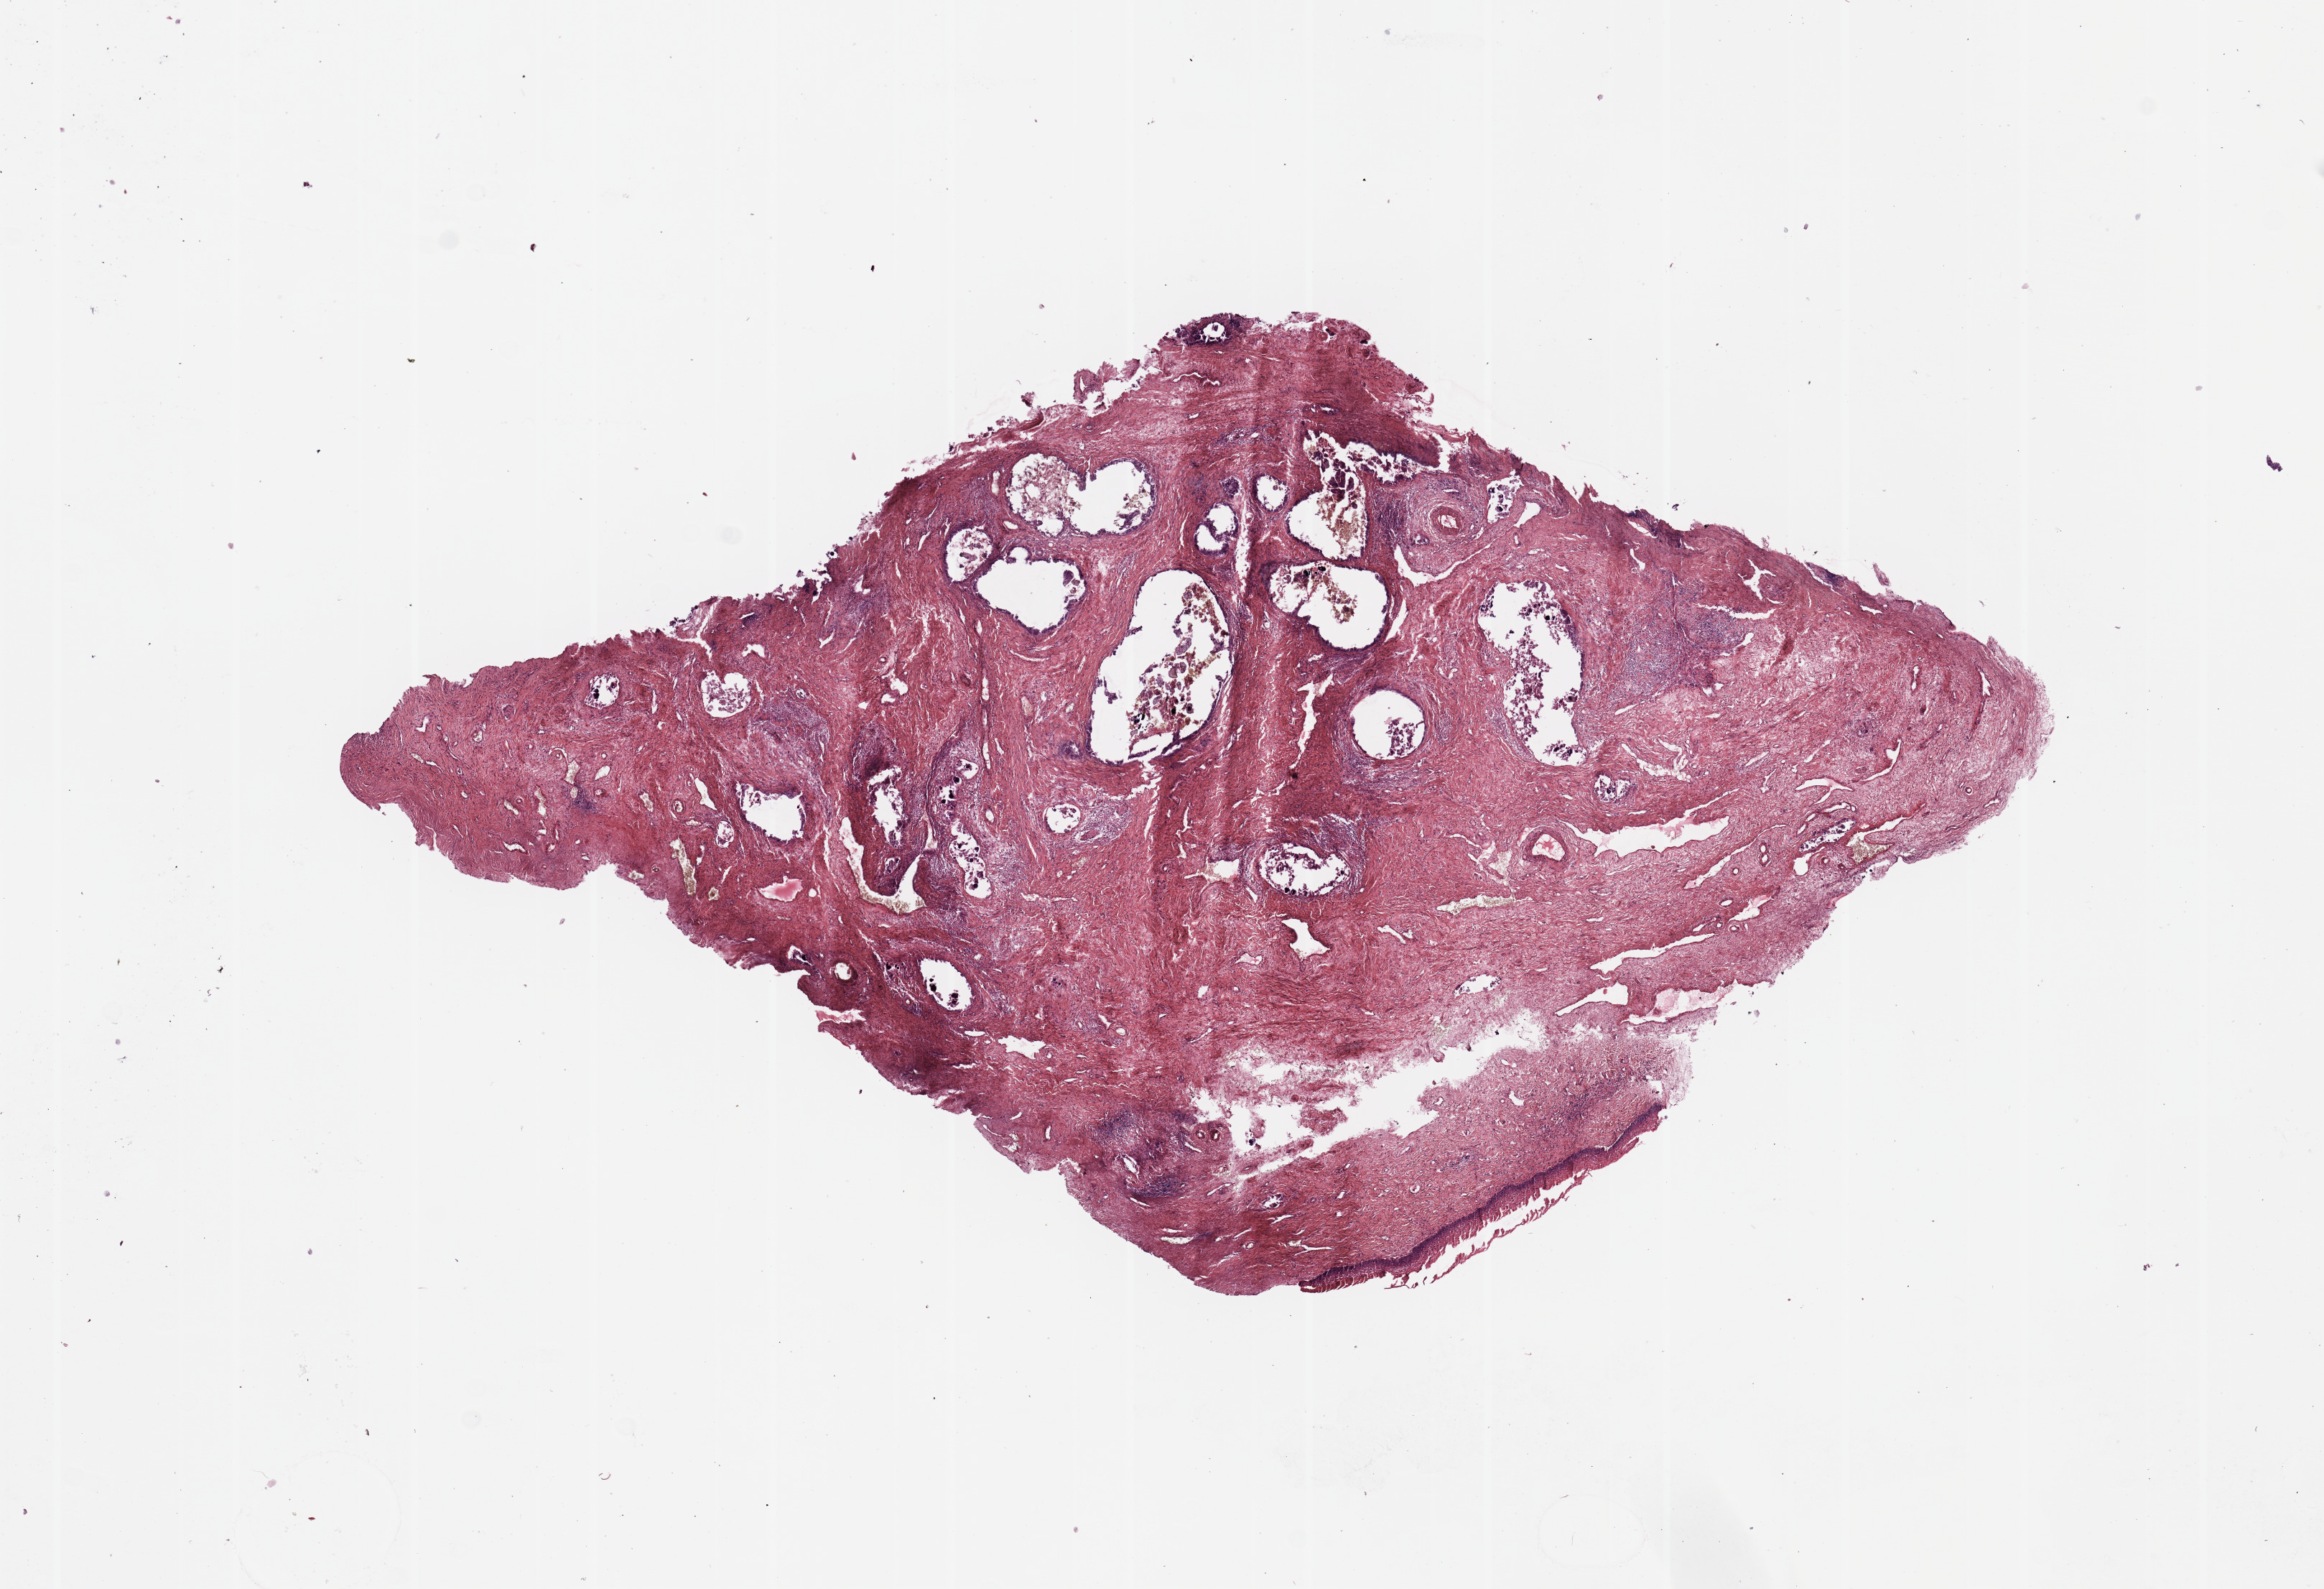
Digitized Hematoxylin and eosin (H&E) stained tissue section (whole slide) — a low-resolution overview of the entire scanned area, about 12.8 x 8.7 mm (acquisition: 20x scan); normal (non-tumour) tissue sample, uterus. Patient: female, age 70 years.
This section: normal (non-tumour) tissue from the same patient. Patient diagnosis: Endometrioid adenocarcinoma, NOS.